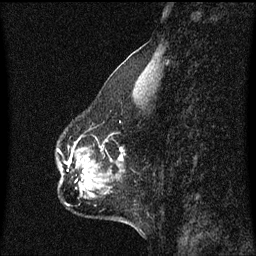
Breast MRI (dynamic contrast-enhanced), one sagittal slice. Slice 21 of 60 in the series (ordered by position). Dynamic contrast-enhanced series, image 2 of 3 at this slice position (ordered by acquisition). 1.5 T. TE 4.2 ms, TR 8.4 ms. 256 × 256 image matrix, field of view 200 × 200 mm. Patient: female, 50 years. Case-level facts recorded for this patient, not image findings: setting: breast cancer imaged before/during neoadjuvant chemotherapy; receptor status: HR-positive, HER2-negative.
Annotated regions visible in this slice (semi-automatic segmentation, software-assisted and operator-edited):
- analysis volume of interest (the breast-tissue region the enhancement analysis was run in; not a lesion): box from (x=59, y=146) to (x=120, y=191) px
- tumour enhancement mask (voxels above the 70 % enhancement threshold inside the analysis volume of interest): (x=84, y=170)–(x=87, y=173)